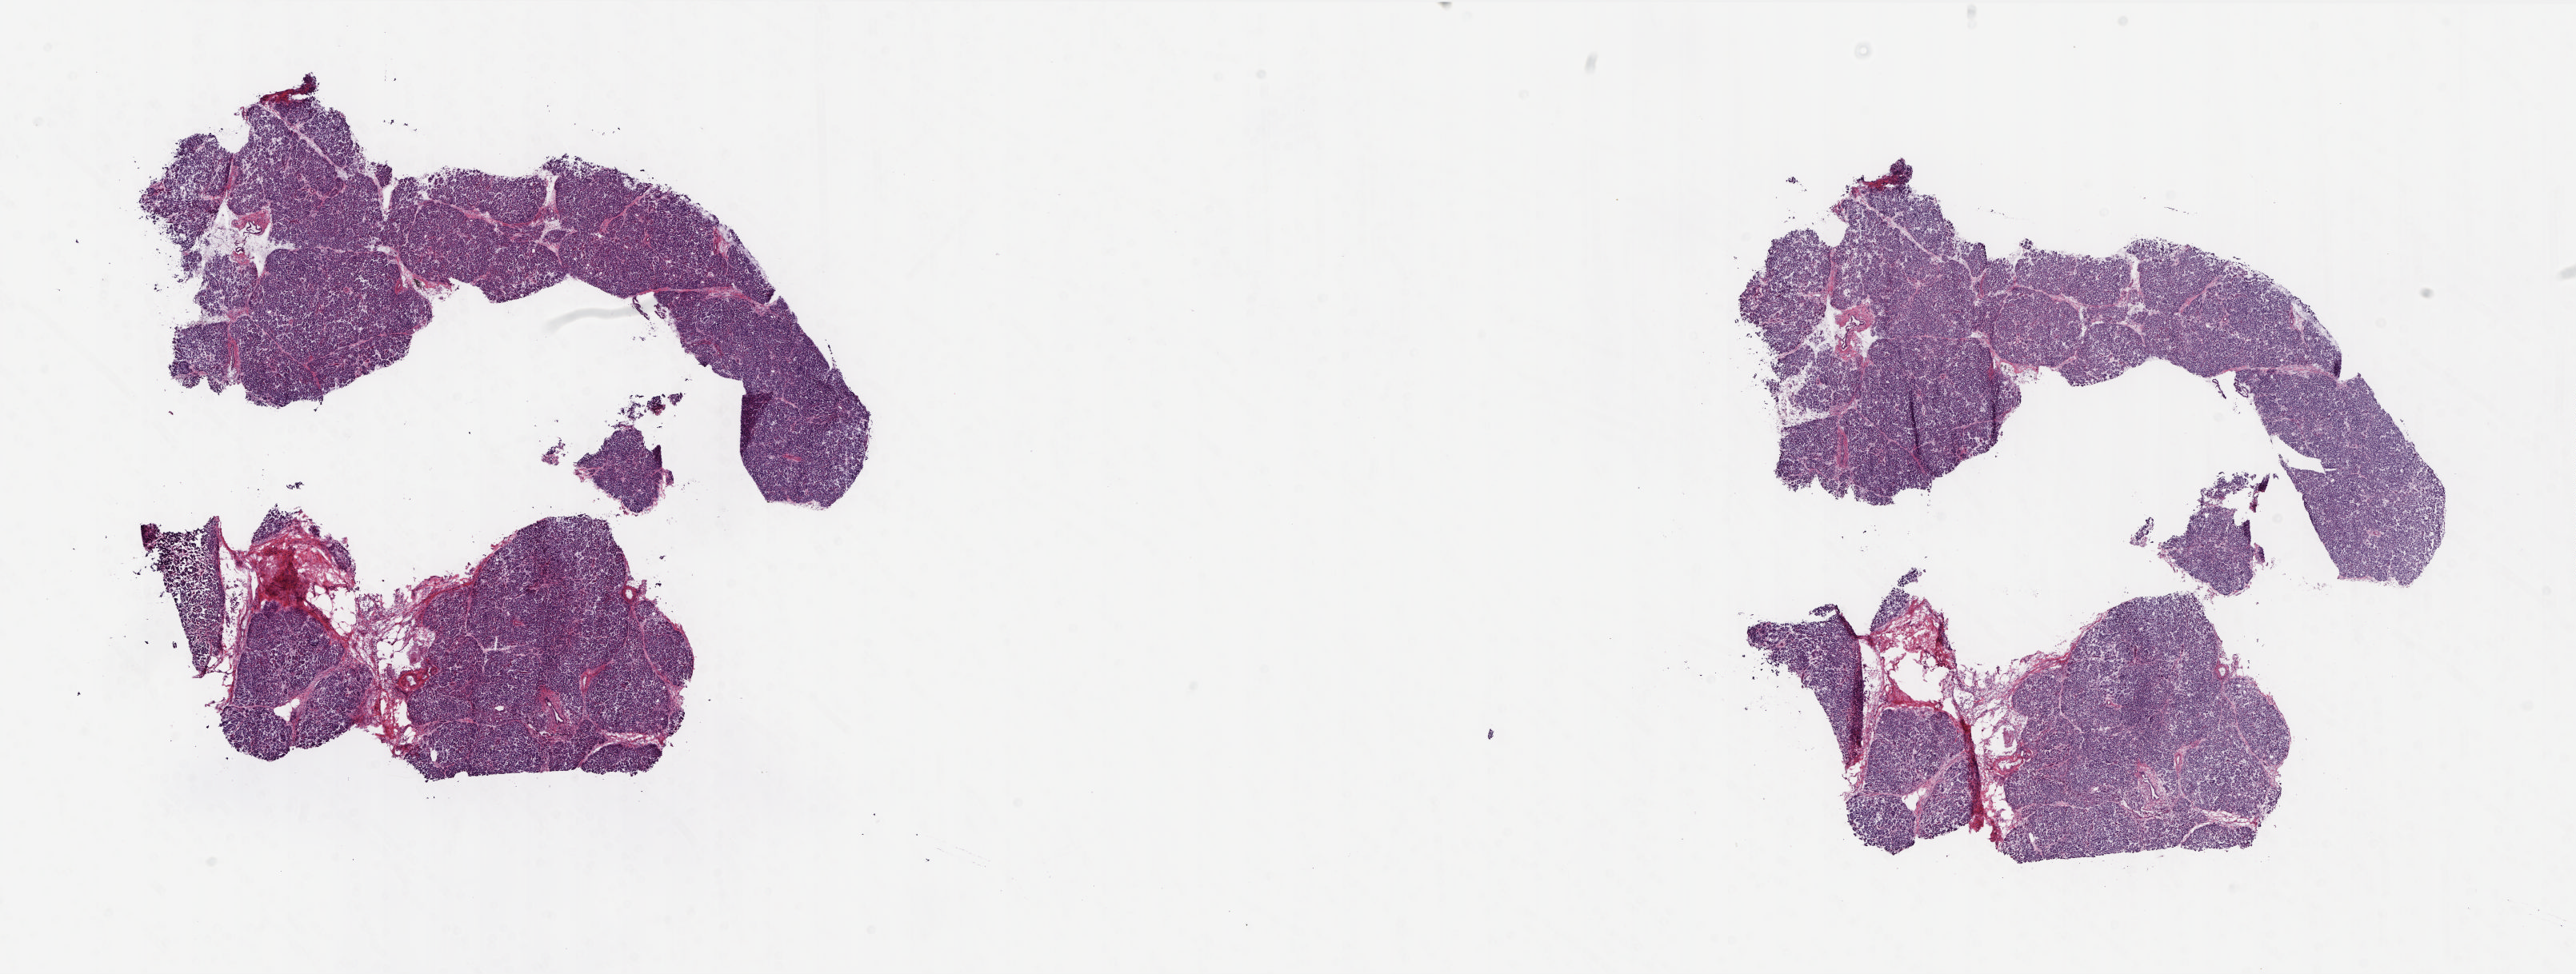
Whole-slide histology image, Hematoxylin and eosin (H&E) stained — low-resolution overview of the scanned area, about 26.0 x 9.8 mm (slide scanned at 20x). Frozen section. Sample: solid tissue normal (non-tumour tissue), pancreas. Female patient; age at initial diagnosis 44 years. Composition of this section per pathologist review: tumour cells 0%, tumour nuclei 0%, normal cells 100%, stromal cells 0%, necrosis 0%. Inflammatory infiltration, as recorded: lymphocyte infiltration 1%, monocyte infiltration 0%, neutrophil infiltration 0%.
This section: solid tissue normal (non-tumour) sample from the same patient. Patient diagnosis: Infiltrating duct carcinoma, NOS (head of pancreas).